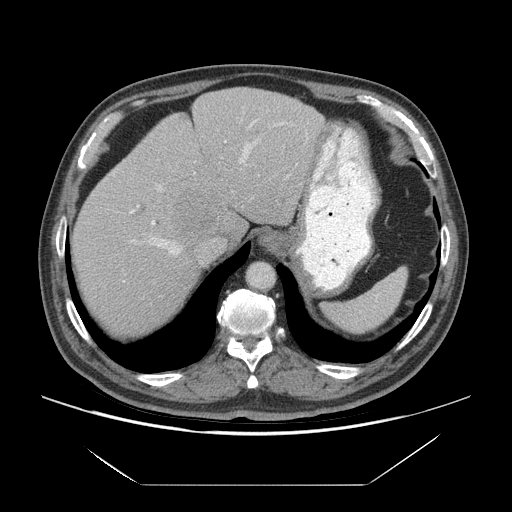
Contrast-enhanced abdominal CT (liver protocol), one axial slice; position 53 of 75 along the scan axis; reconstruction kernel STANDARD; soft-tissue window (W 400 / L 40 HU); 2.5 mm slice thickness; 512 × 512 image matrix, field of view 420 × 420 mm. From the clinical record (not read from this slice): diagnosis: hepatocellular carcinoma (patient treated with transarterial chemoembolisation; whether this scan precedes or follows treatment is not stated here); TNM stage (as recorded): Stage-I.
Outlined on this slice (semi-automatically segmented with operator editing):
- abdominal aorta: bounding box [x1, y1, x2, y2] px = [248, 263, 274, 289]
- liver parenchyma outside the tumour (the mass and vessels are separate outlines, so this box may not span the whole liver): [70, 88, 324, 334]
- mass: [170, 186, 219, 239]
- liver vessels: [114, 119, 308, 254]